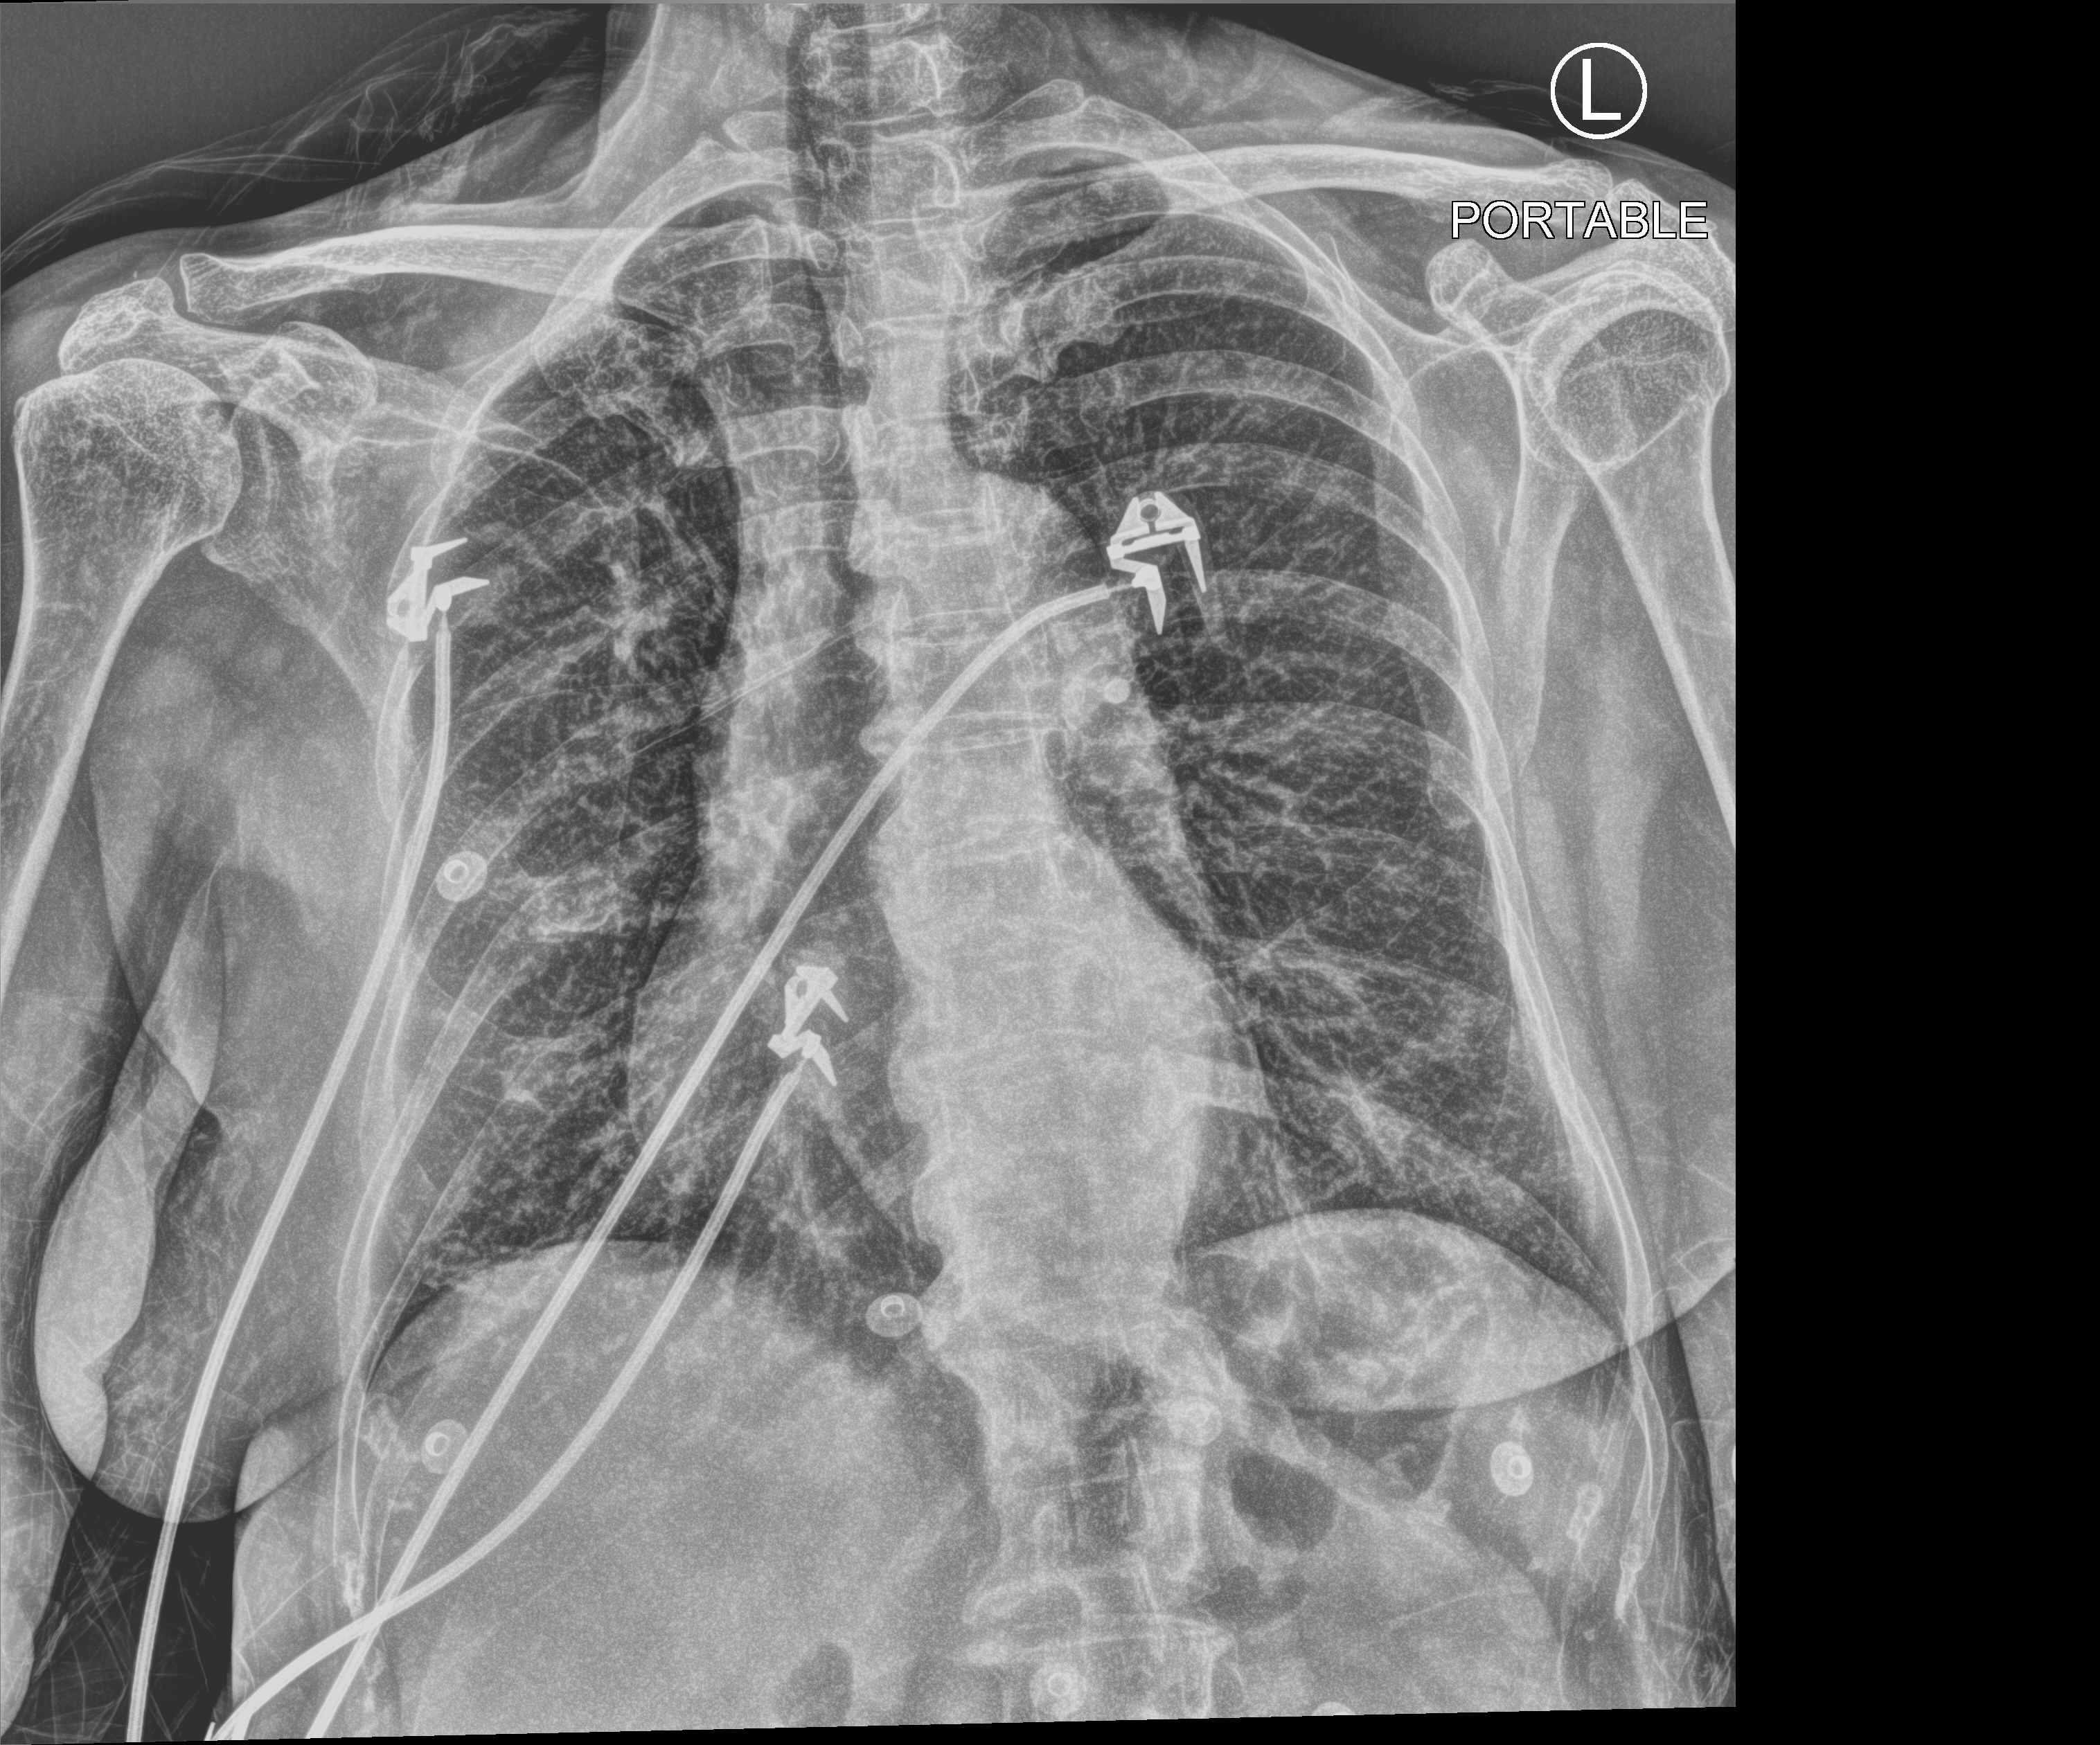
Portable chest radiograph; anteroposterior (AP) projection. Female patient hospitalised with COVID-19, age 60–74 years.
Hospital-stay facts (about this admission, not read from this image; timing relative to this image not recorded): other chronic lung disease (admission record): no.